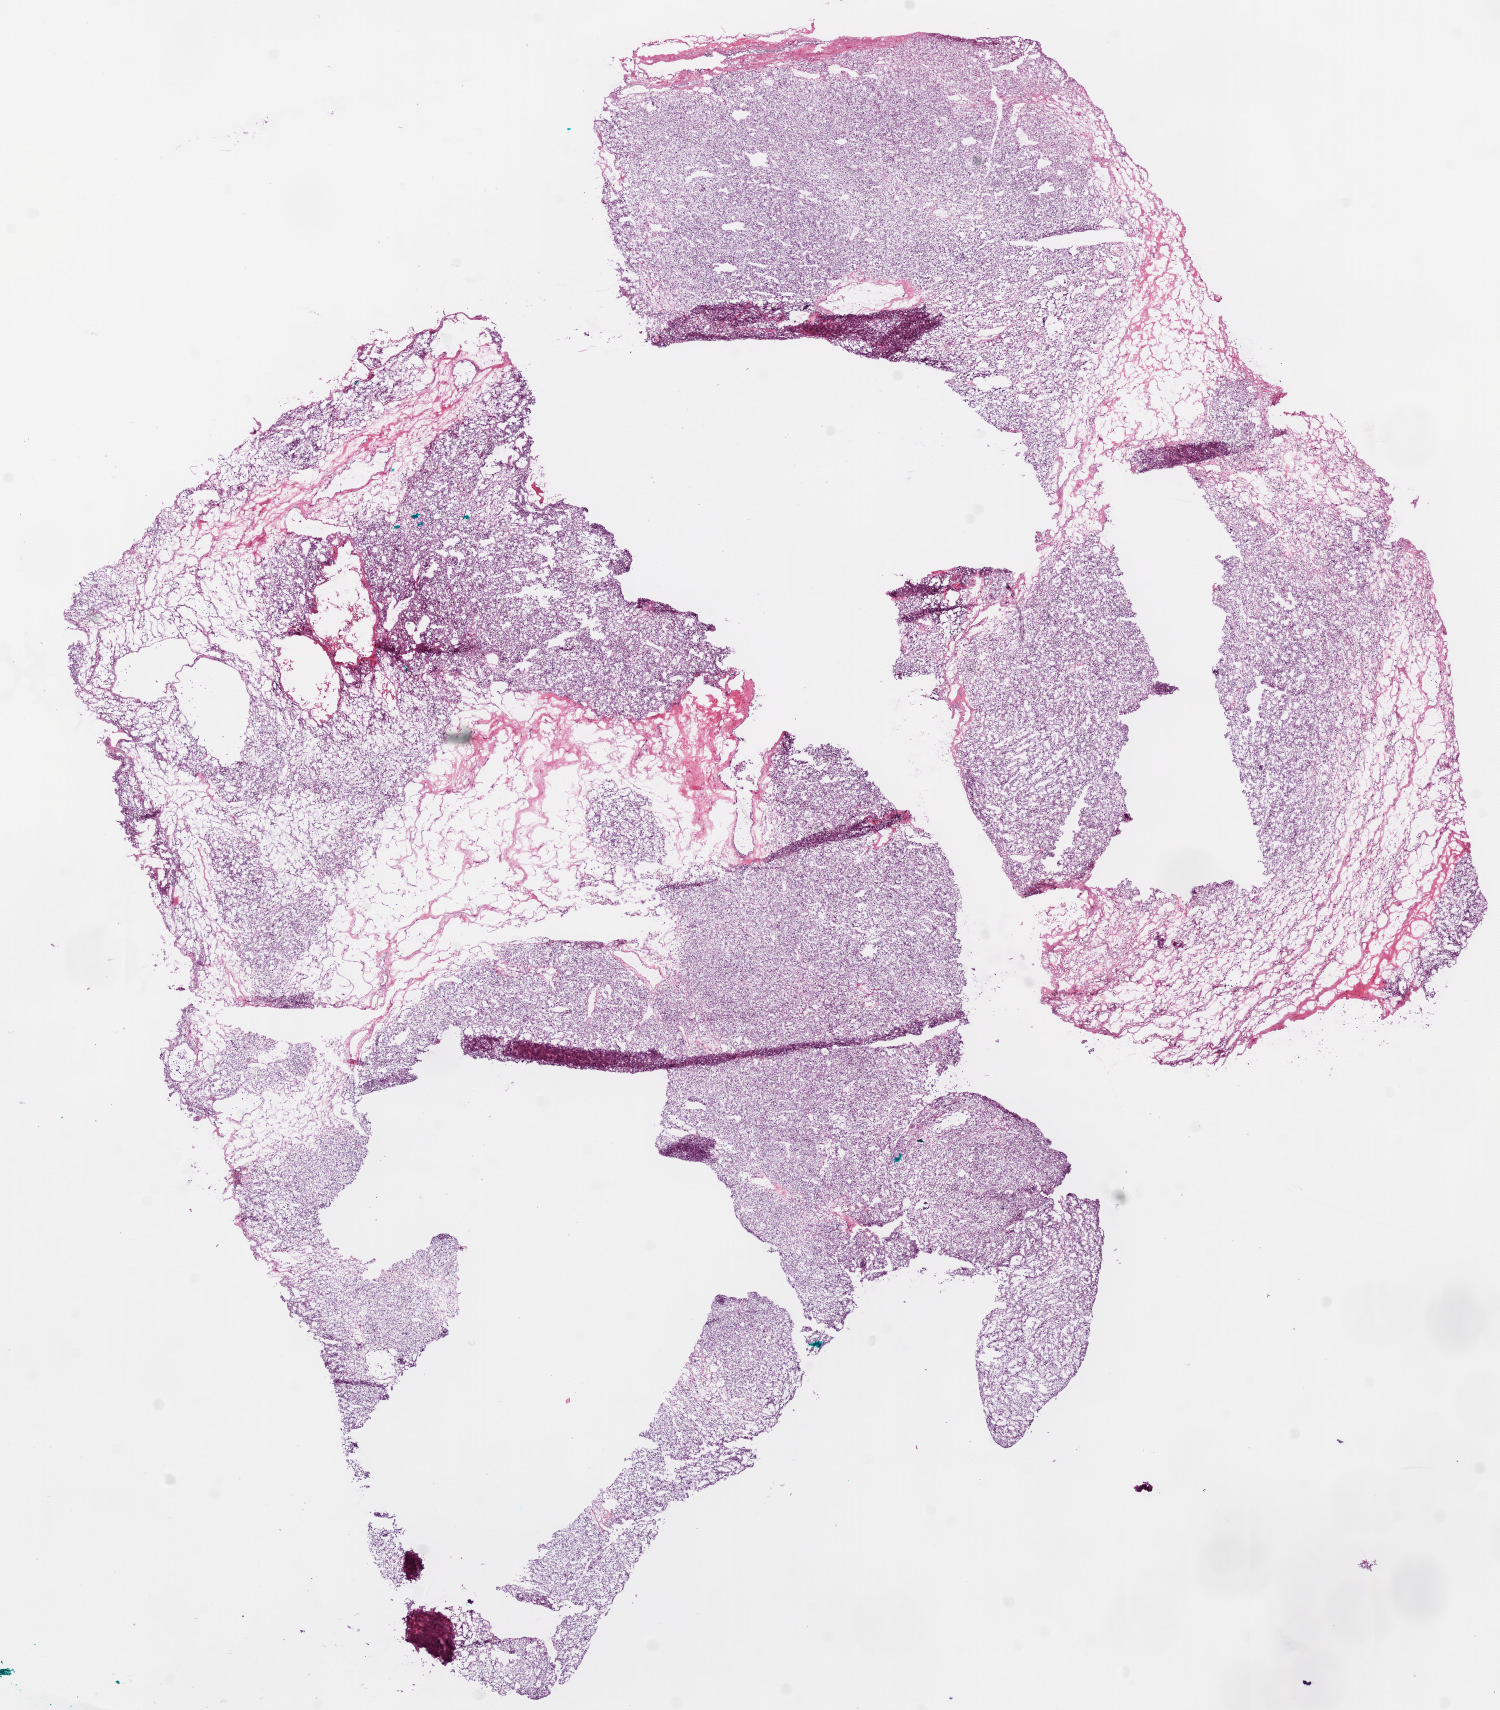
H&E whole-slide image, whole scanned area (about 12.0 x 13.7 mm) shown as a low-resolution overview, frozen section, sample: primary tumour, kidney. Patient sex: female. Histologic grade: G2 (moderately differentiated). Pathologist review of this section (percent, as recorded): tumour cells 85%, tumour nuclei 80%, normal cells 0%, stromal cells 15%, necrosis 0%.
Diagnosis: Clear cell adenocarcinoma, NOS. Laterality: right. AJCC pathologic stage: I (6th edition).